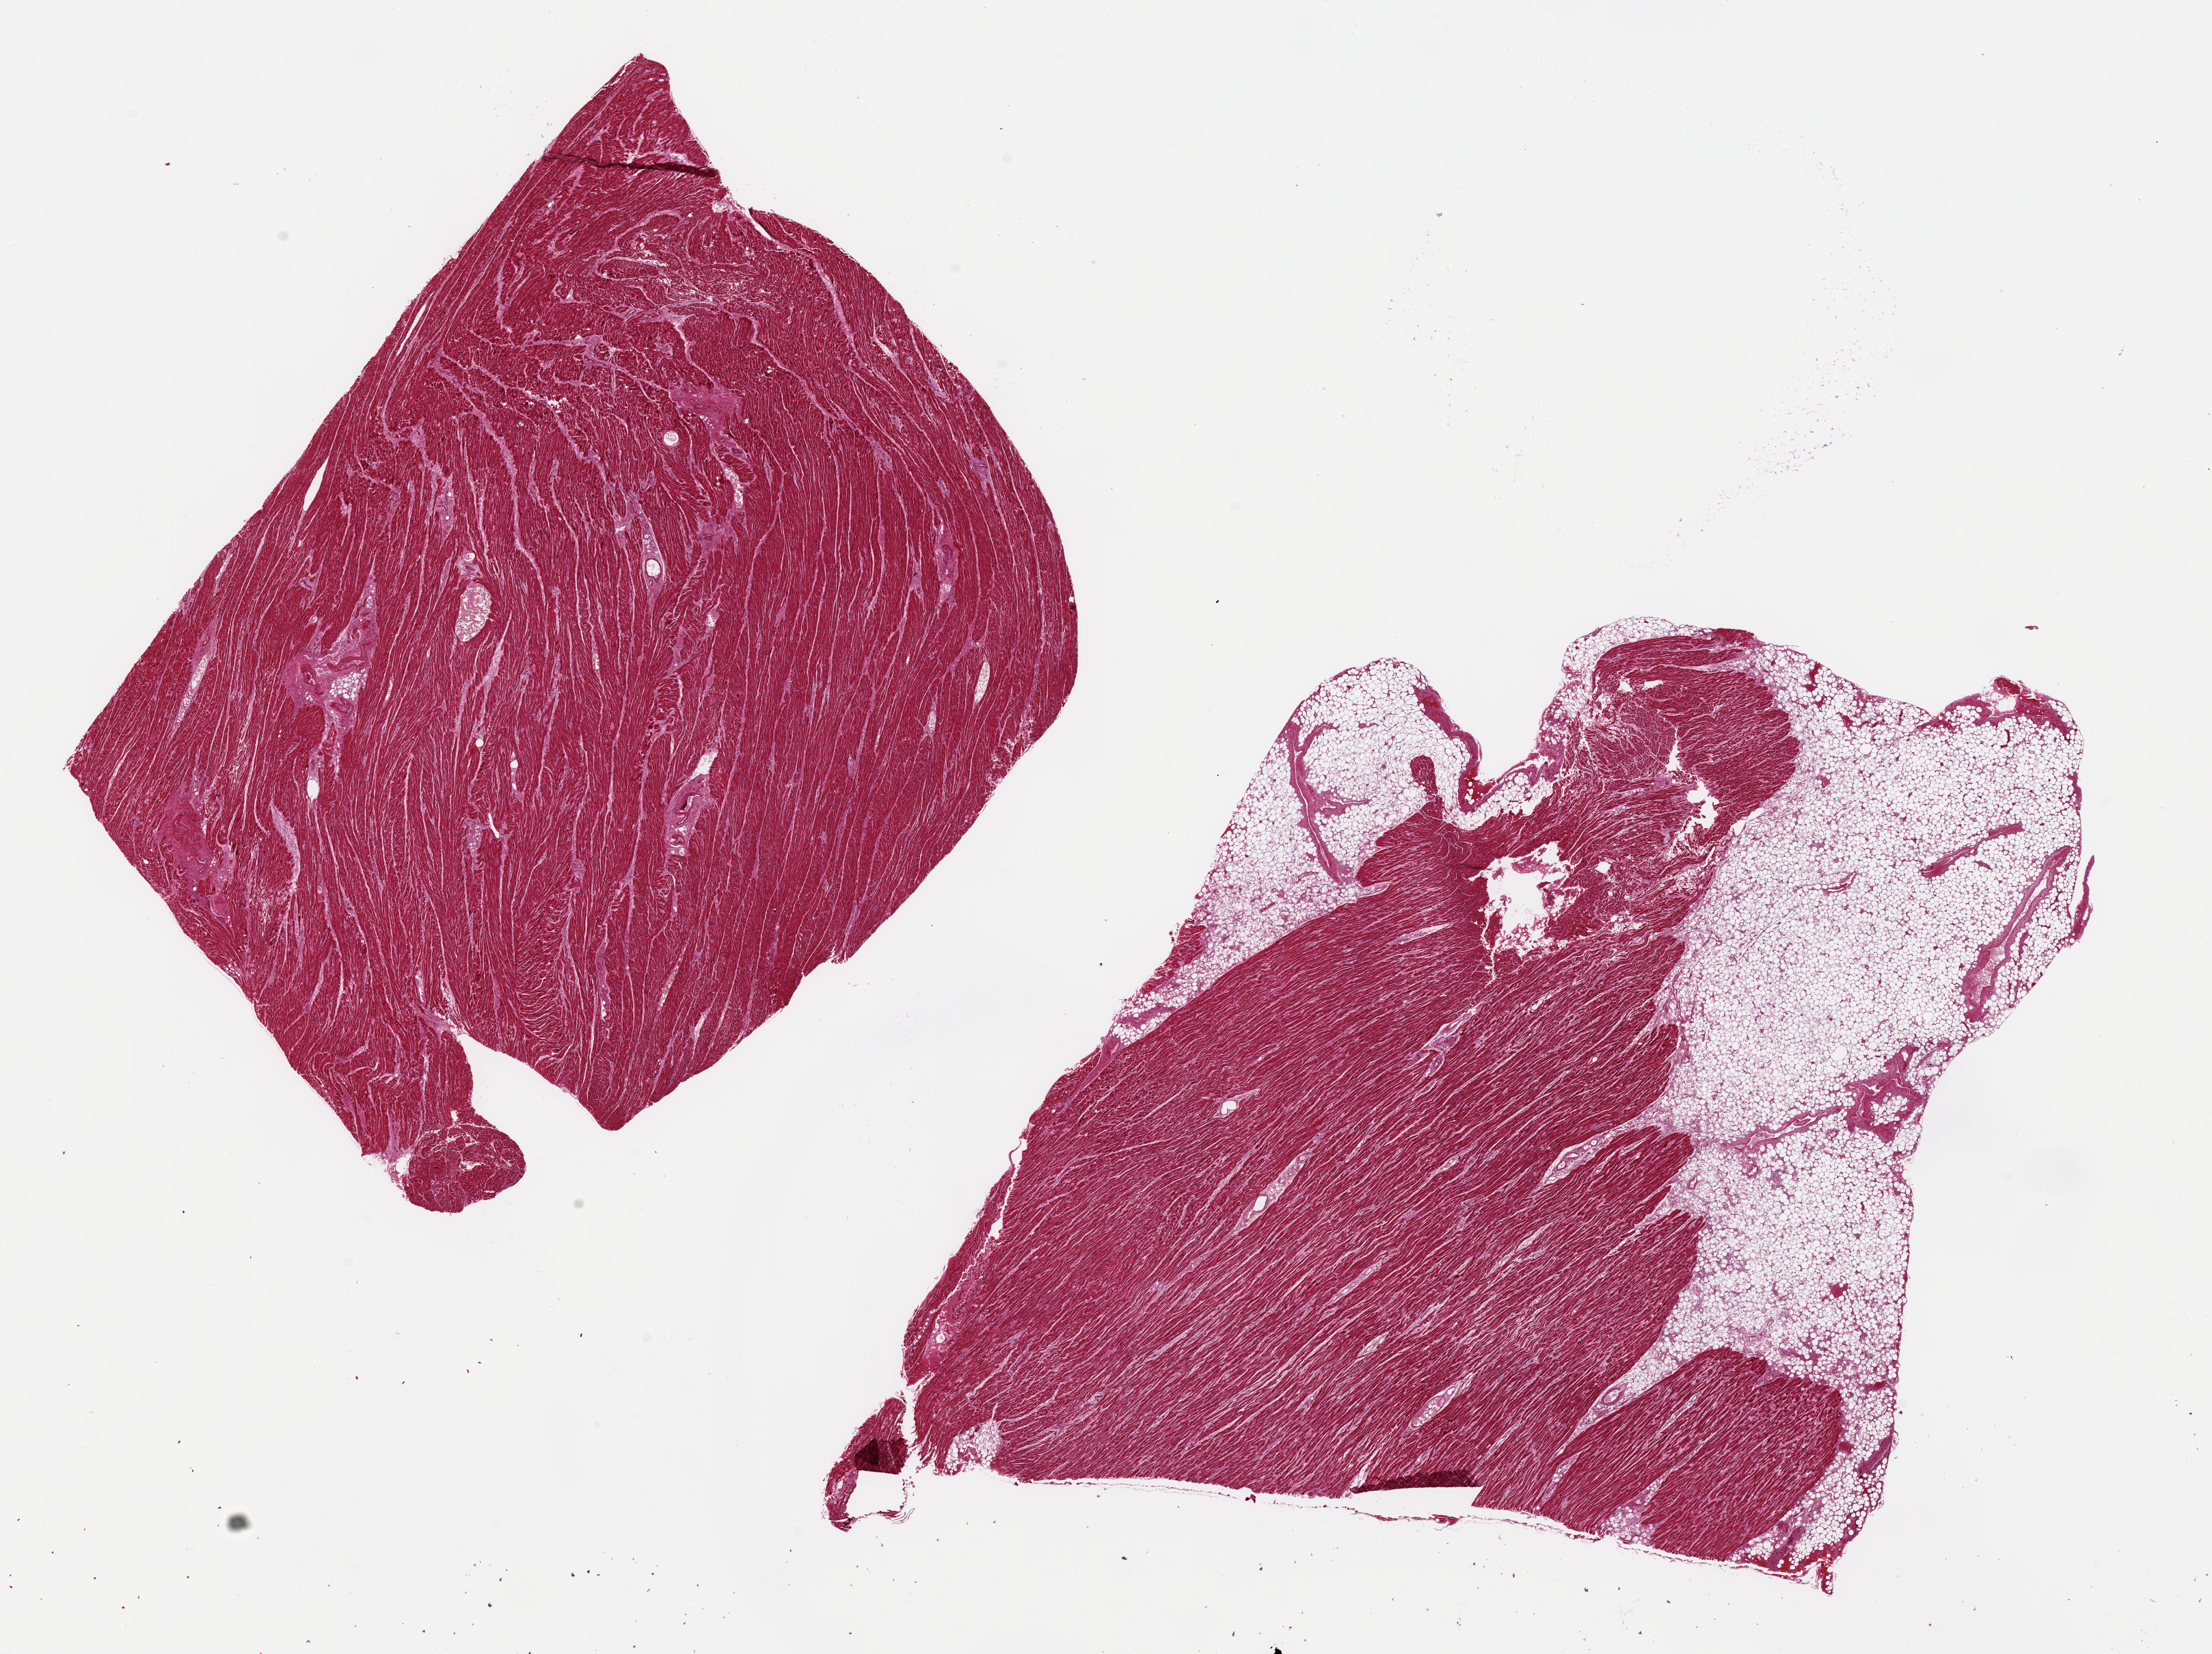
Whole-slide image, haematoxylin and eosin stain — low-resolution overview of the scanned area, about 25.6 x 19.1 mm (slide scanned at 20x), PAXgene-fixed paraffin-embedded (PFPE) section, section of heart (target tissue), tissue donor sample. Female donor.
Review note (as recorded): 2 ~10x10mm aliquots, one ~25% attached adipose pericardial fat (10x5mm).